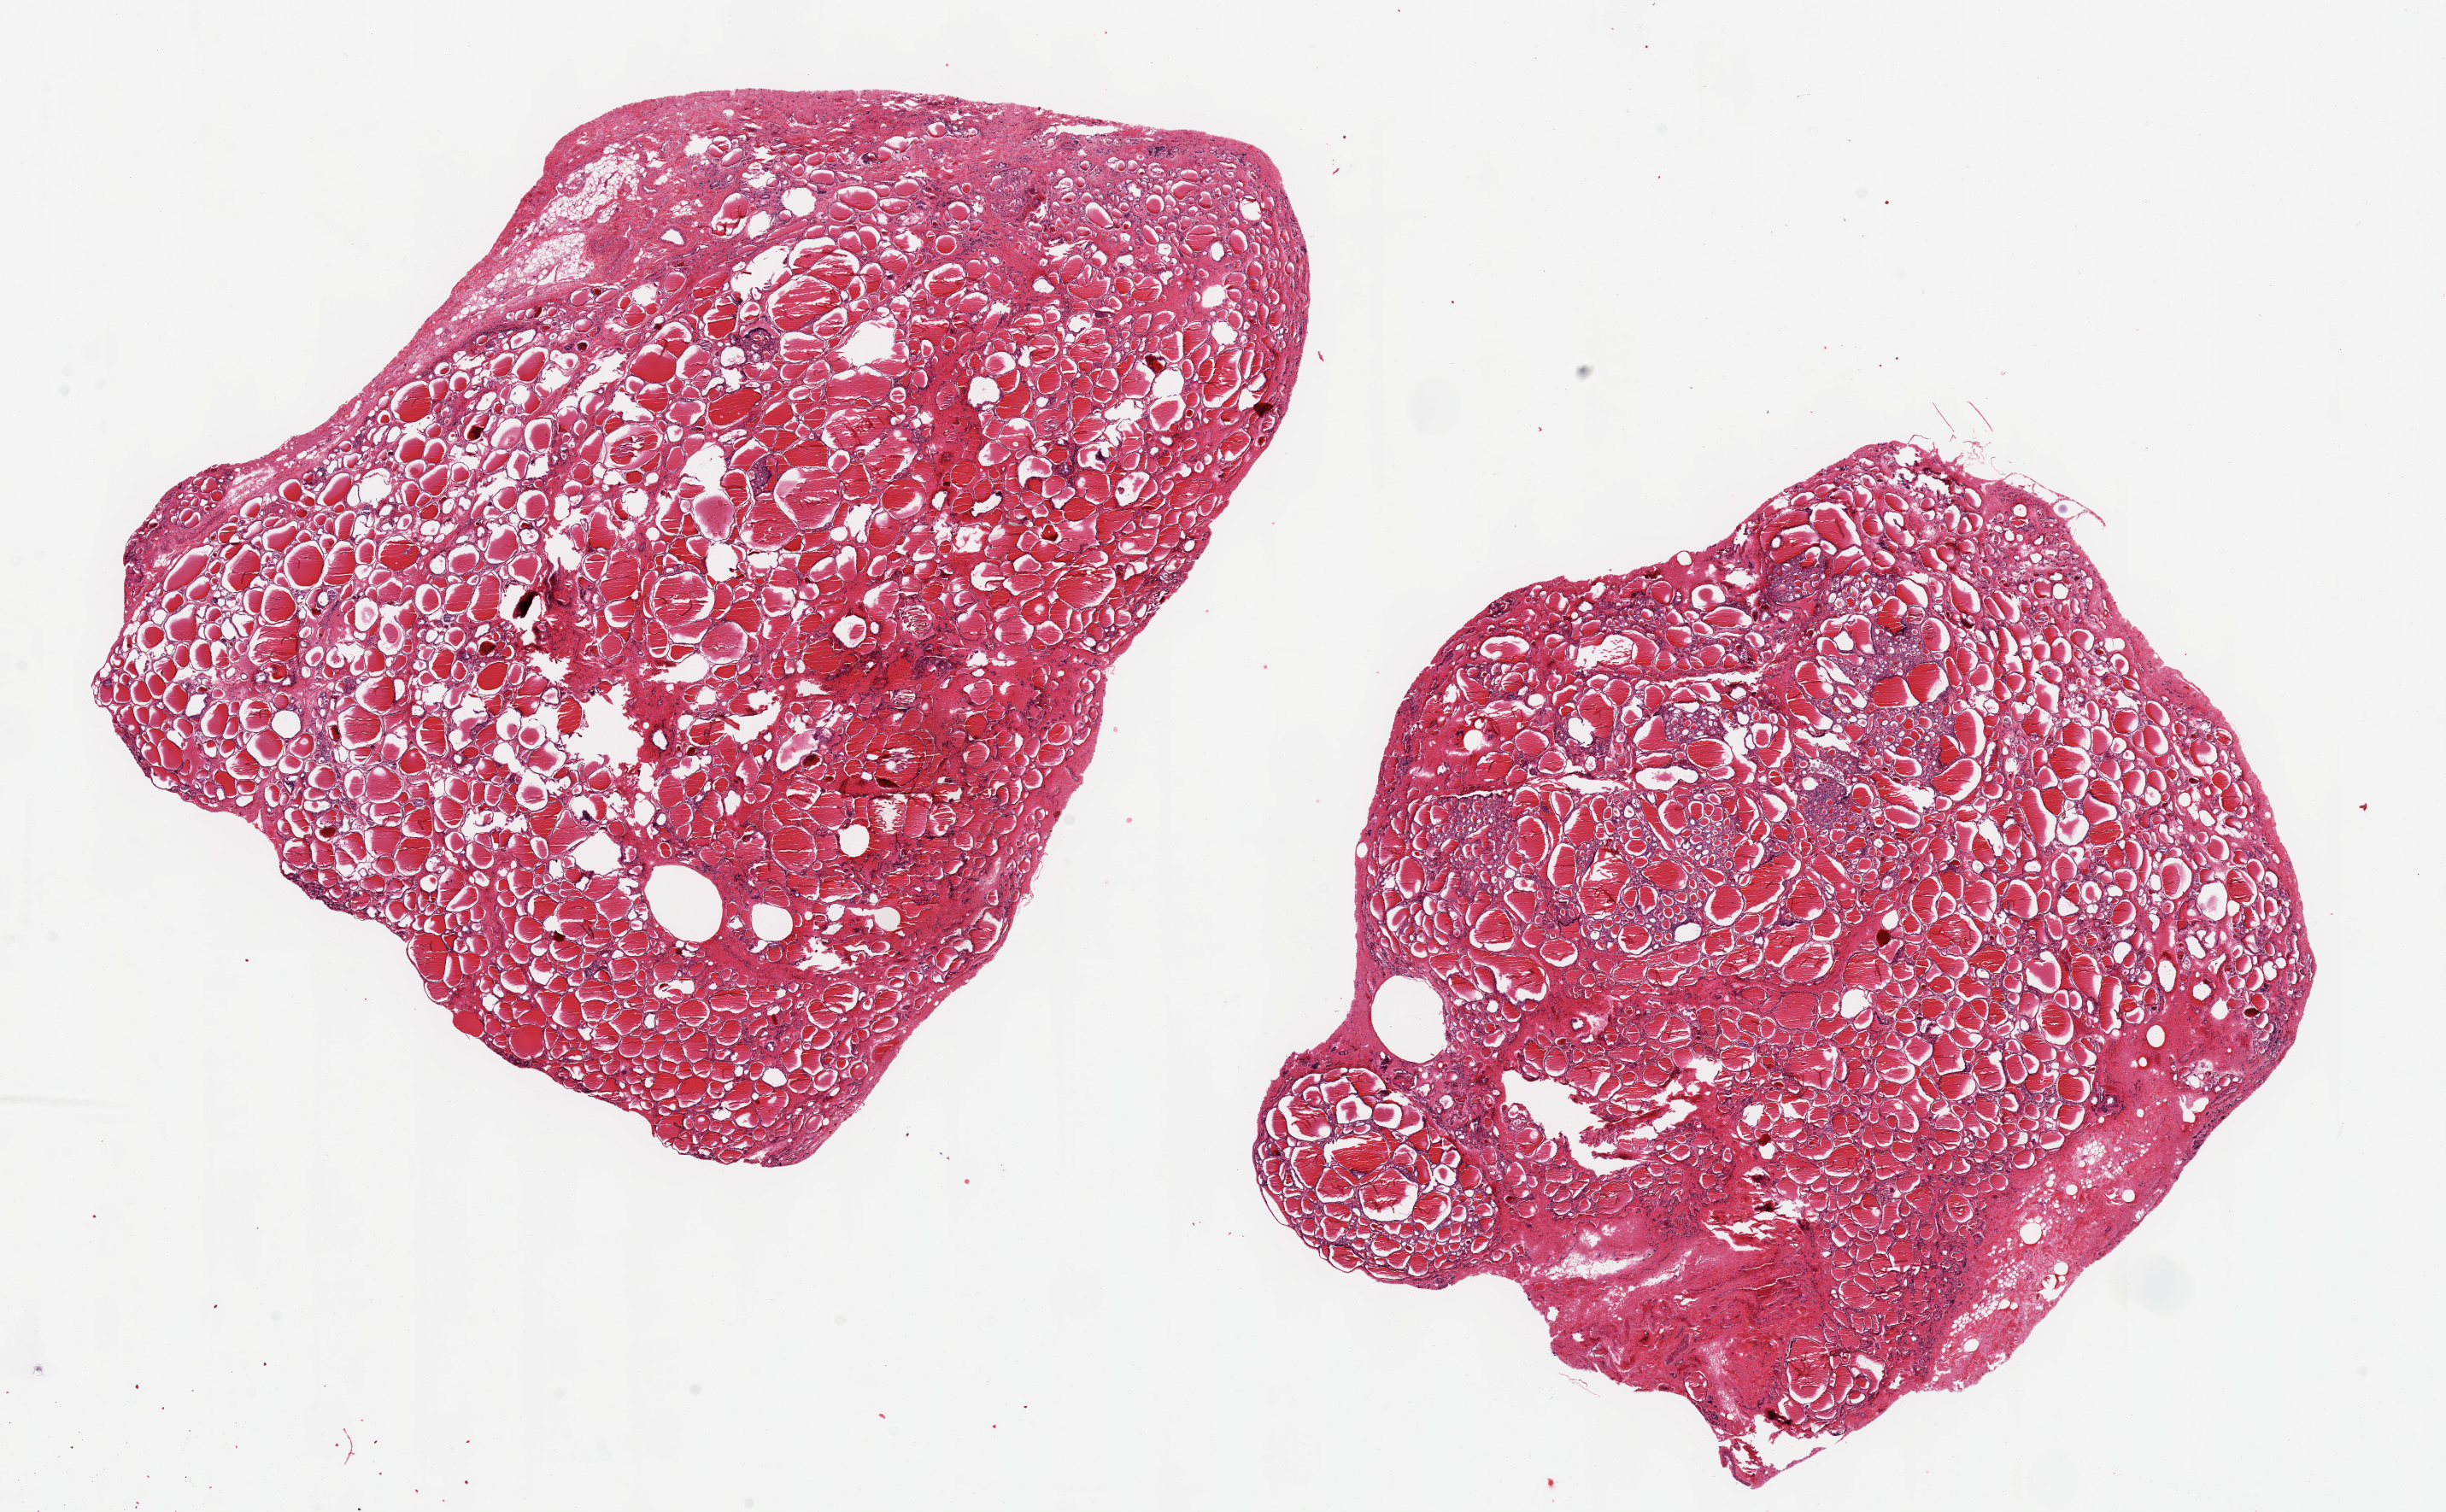
Hematoxylin and eosin (H&E) whole-slide image, brightfield — whole scanned area (about 22.6 x 14.0 mm, slide scanned at 20x) shown as a low-resolution overview, PAXgene-fixed paraffin-embedded (PFPE) section, sampled site (target tissue): thyroid, donor tissue sample. Donor: male.
• reviewer comment on this tissue sample: 2 ~9.5x8mm pieces